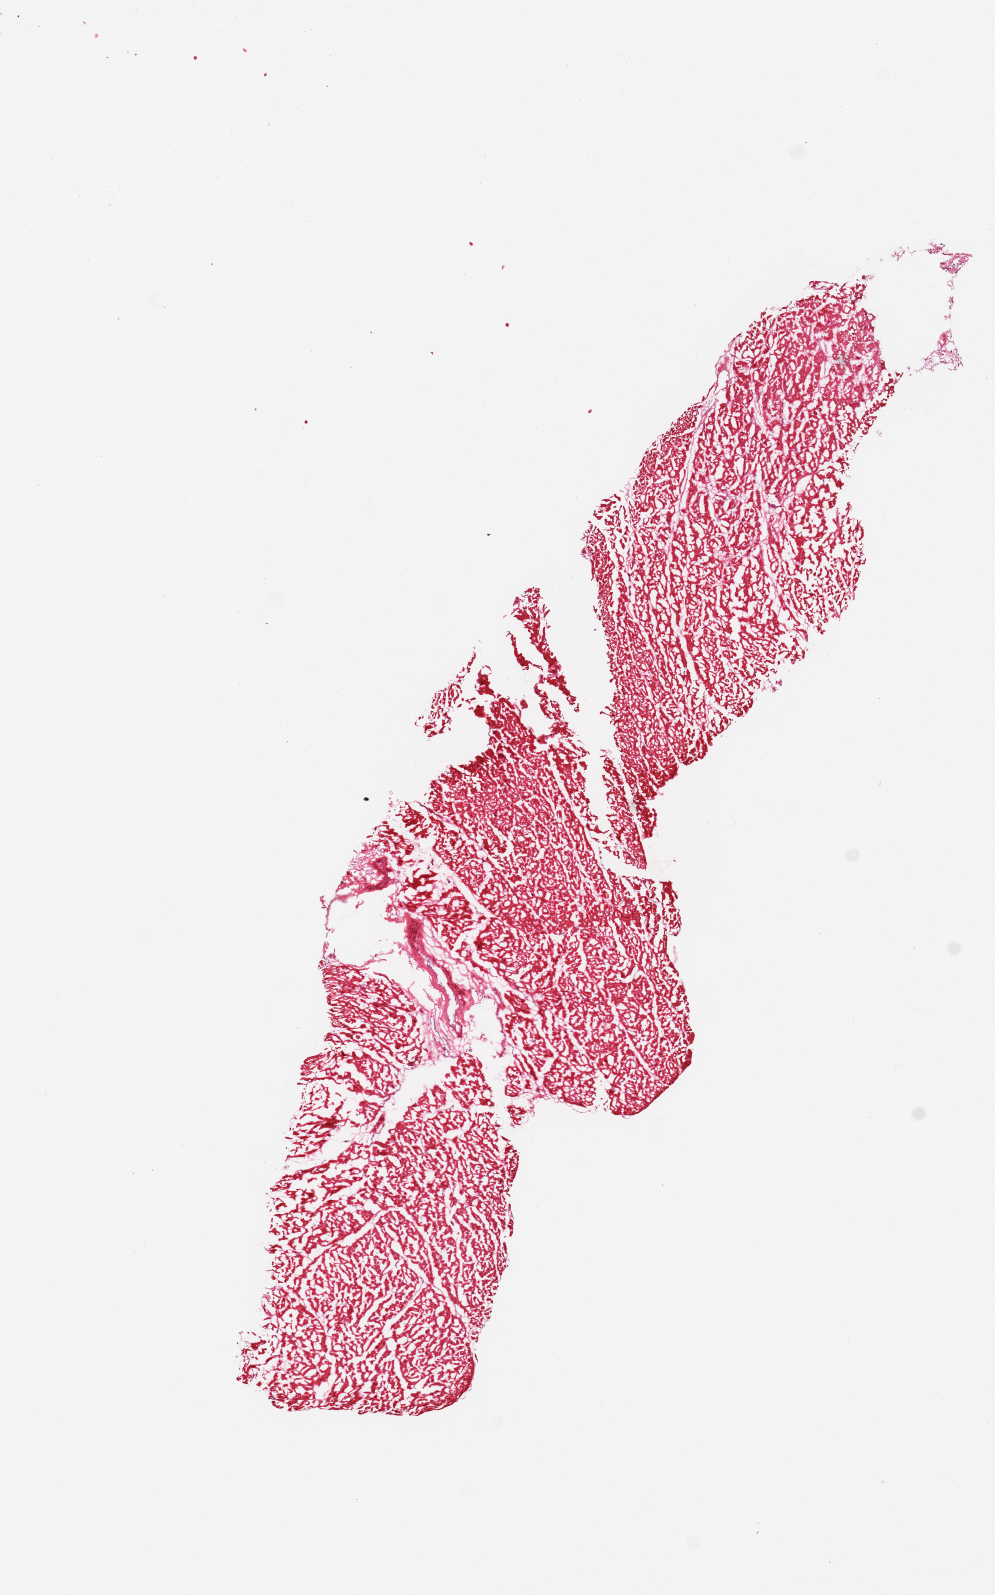
Digitized haematoxylin and eosin-stained section, shown as a low-resolution overview of the whole scanned area (about 7.9 x 12.6 mm, from a 20x scan). Male donor.
Specimen: frozen section (dry ice); section of heart (target tissue); tissue donor sample.